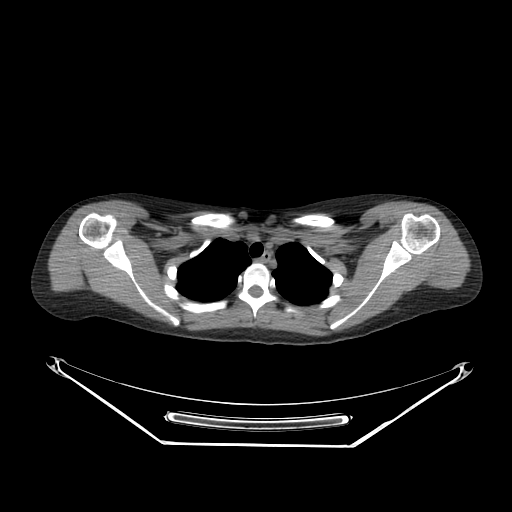
CT of an extremity soft-tissue mass (from a PET/CT study), one axial slice; position 212 of 267 along the scan axis; reconstruction kernel SOFT; 140 kVp; soft-tissue window (W 400 / L 40 HU); 512 × 512 image matrix. Female patient. From the clinical record (not read from this slice): histological type: malignant fibrous histiocytoma; grade: low; site of the primary tumour: left arm.
Outlined on this slice (expert contour drawn on MRI and transferred to this co-registered scan by the dataset authors):
- gross tumour volume (mass): bounding box <429,263,451,280> (left, top, right, bottom; pixels)